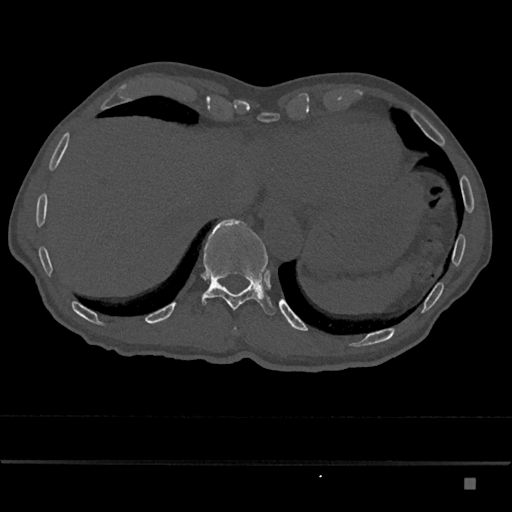
CT including the spine, one axial slice. Slice 682 of 797 in the series (ordered by position). Reconstruction kernel Br40s/3. 120 kVp. Bone window (W 1800 / L 400 HU). 0.5 mm slice thickness. 512 × 512 image matrix, field of view 390 × 390 mm. Patient: male, 72 years. From the clinical record (not read from this slice): primary cancer: prostate.
Structures marked on this image (semi-automatically segmented with operator editing):
- T10 vertebra: bounding box <234,328,236,330> (left, top, right, bottom; pixels)
- T11 vertebra: <202,219,275,315>